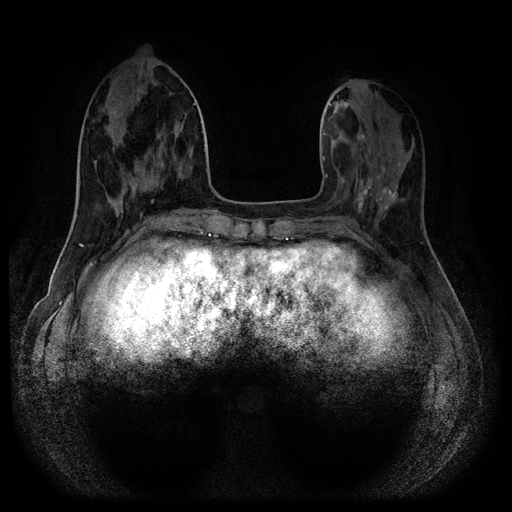
Breast MRI (dynamic contrast-enhanced, multi-phase), one axial slice. Position 39 of 116 along the scan axis. Dynamic contrast-enhanced series, time point 2 of 5 at this slice position (early post-contrast). 1.5 T. TE 2.7 ms, TR 5.4 ms. 2 mm slice thickness. 512 × 512 image matrix. Patient: female, 40 years.
Structures marked on this image (semi-automatic segmentation, software-assisted and operator-edited):
- breast lesion (labelled benign in the annotation): bounding box <354,168,378,215> (left, top, right, bottom; pixels)
- breast lesion (labelled benign in the annotation): <338,100,349,109>